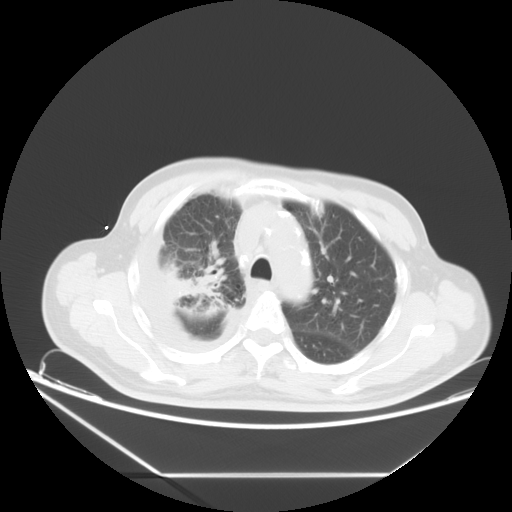
Chest CT, one axial slice; slice 11 of 20 in the series (ordered by position); reconstruction kernel STANDARD; 120 kVp; lung window (W 1500 / L -600 HU); 5 mm slice thickness; 512 × 512 image matrix, field of view 418 × 418 mm. Patient: male, 75 years. From the clinical record (not read from this slice): clinical TNM (as recorded): T1c N1 M1.
Annotated regions visible in this slice (rectangle marked by the reading radiologist):
- lung tumour (recorded histology: adenocarcinoma): bounding box (x1, y1, x2, y2) in pixels: (166, 263, 225, 307)